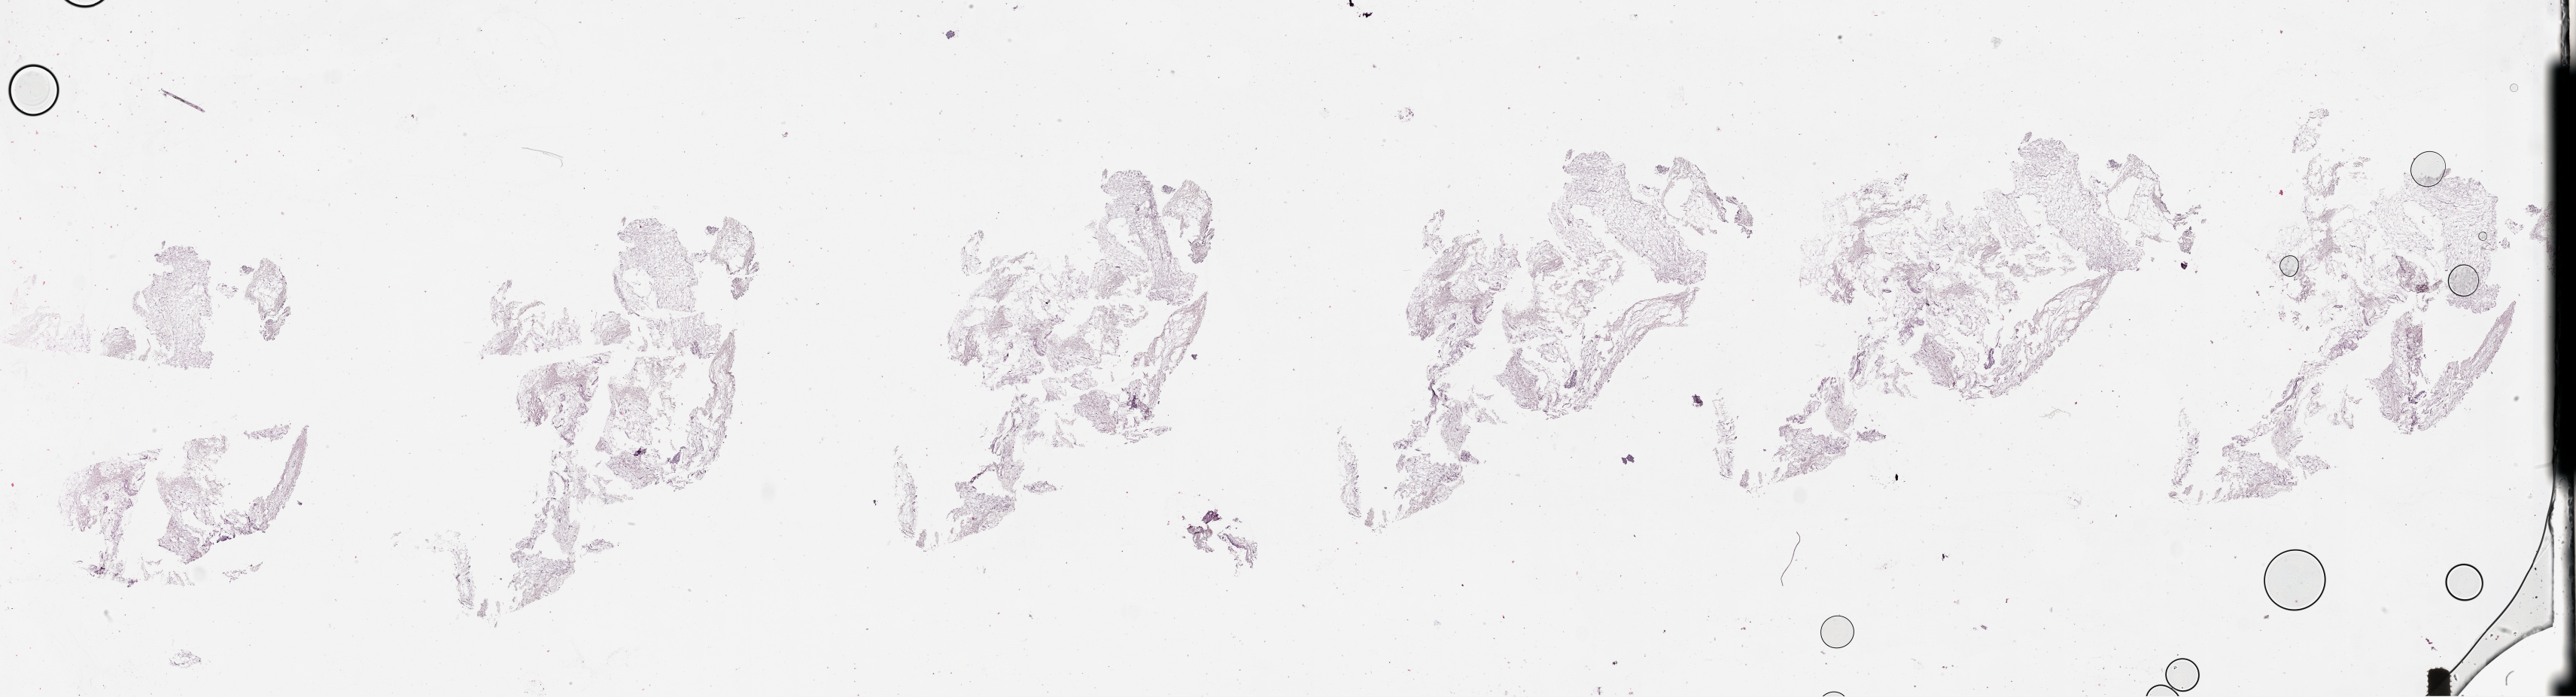
Whole-slide histology image, Hematoxylin and eosin (H&E) stained — whole scanned area (about 55.1 x 14.9 mm, from a 20x scan) shown as a low-resolution overview. 70-year-old female patient.
Patient diagnosis: Malignant melanoma, NOS.